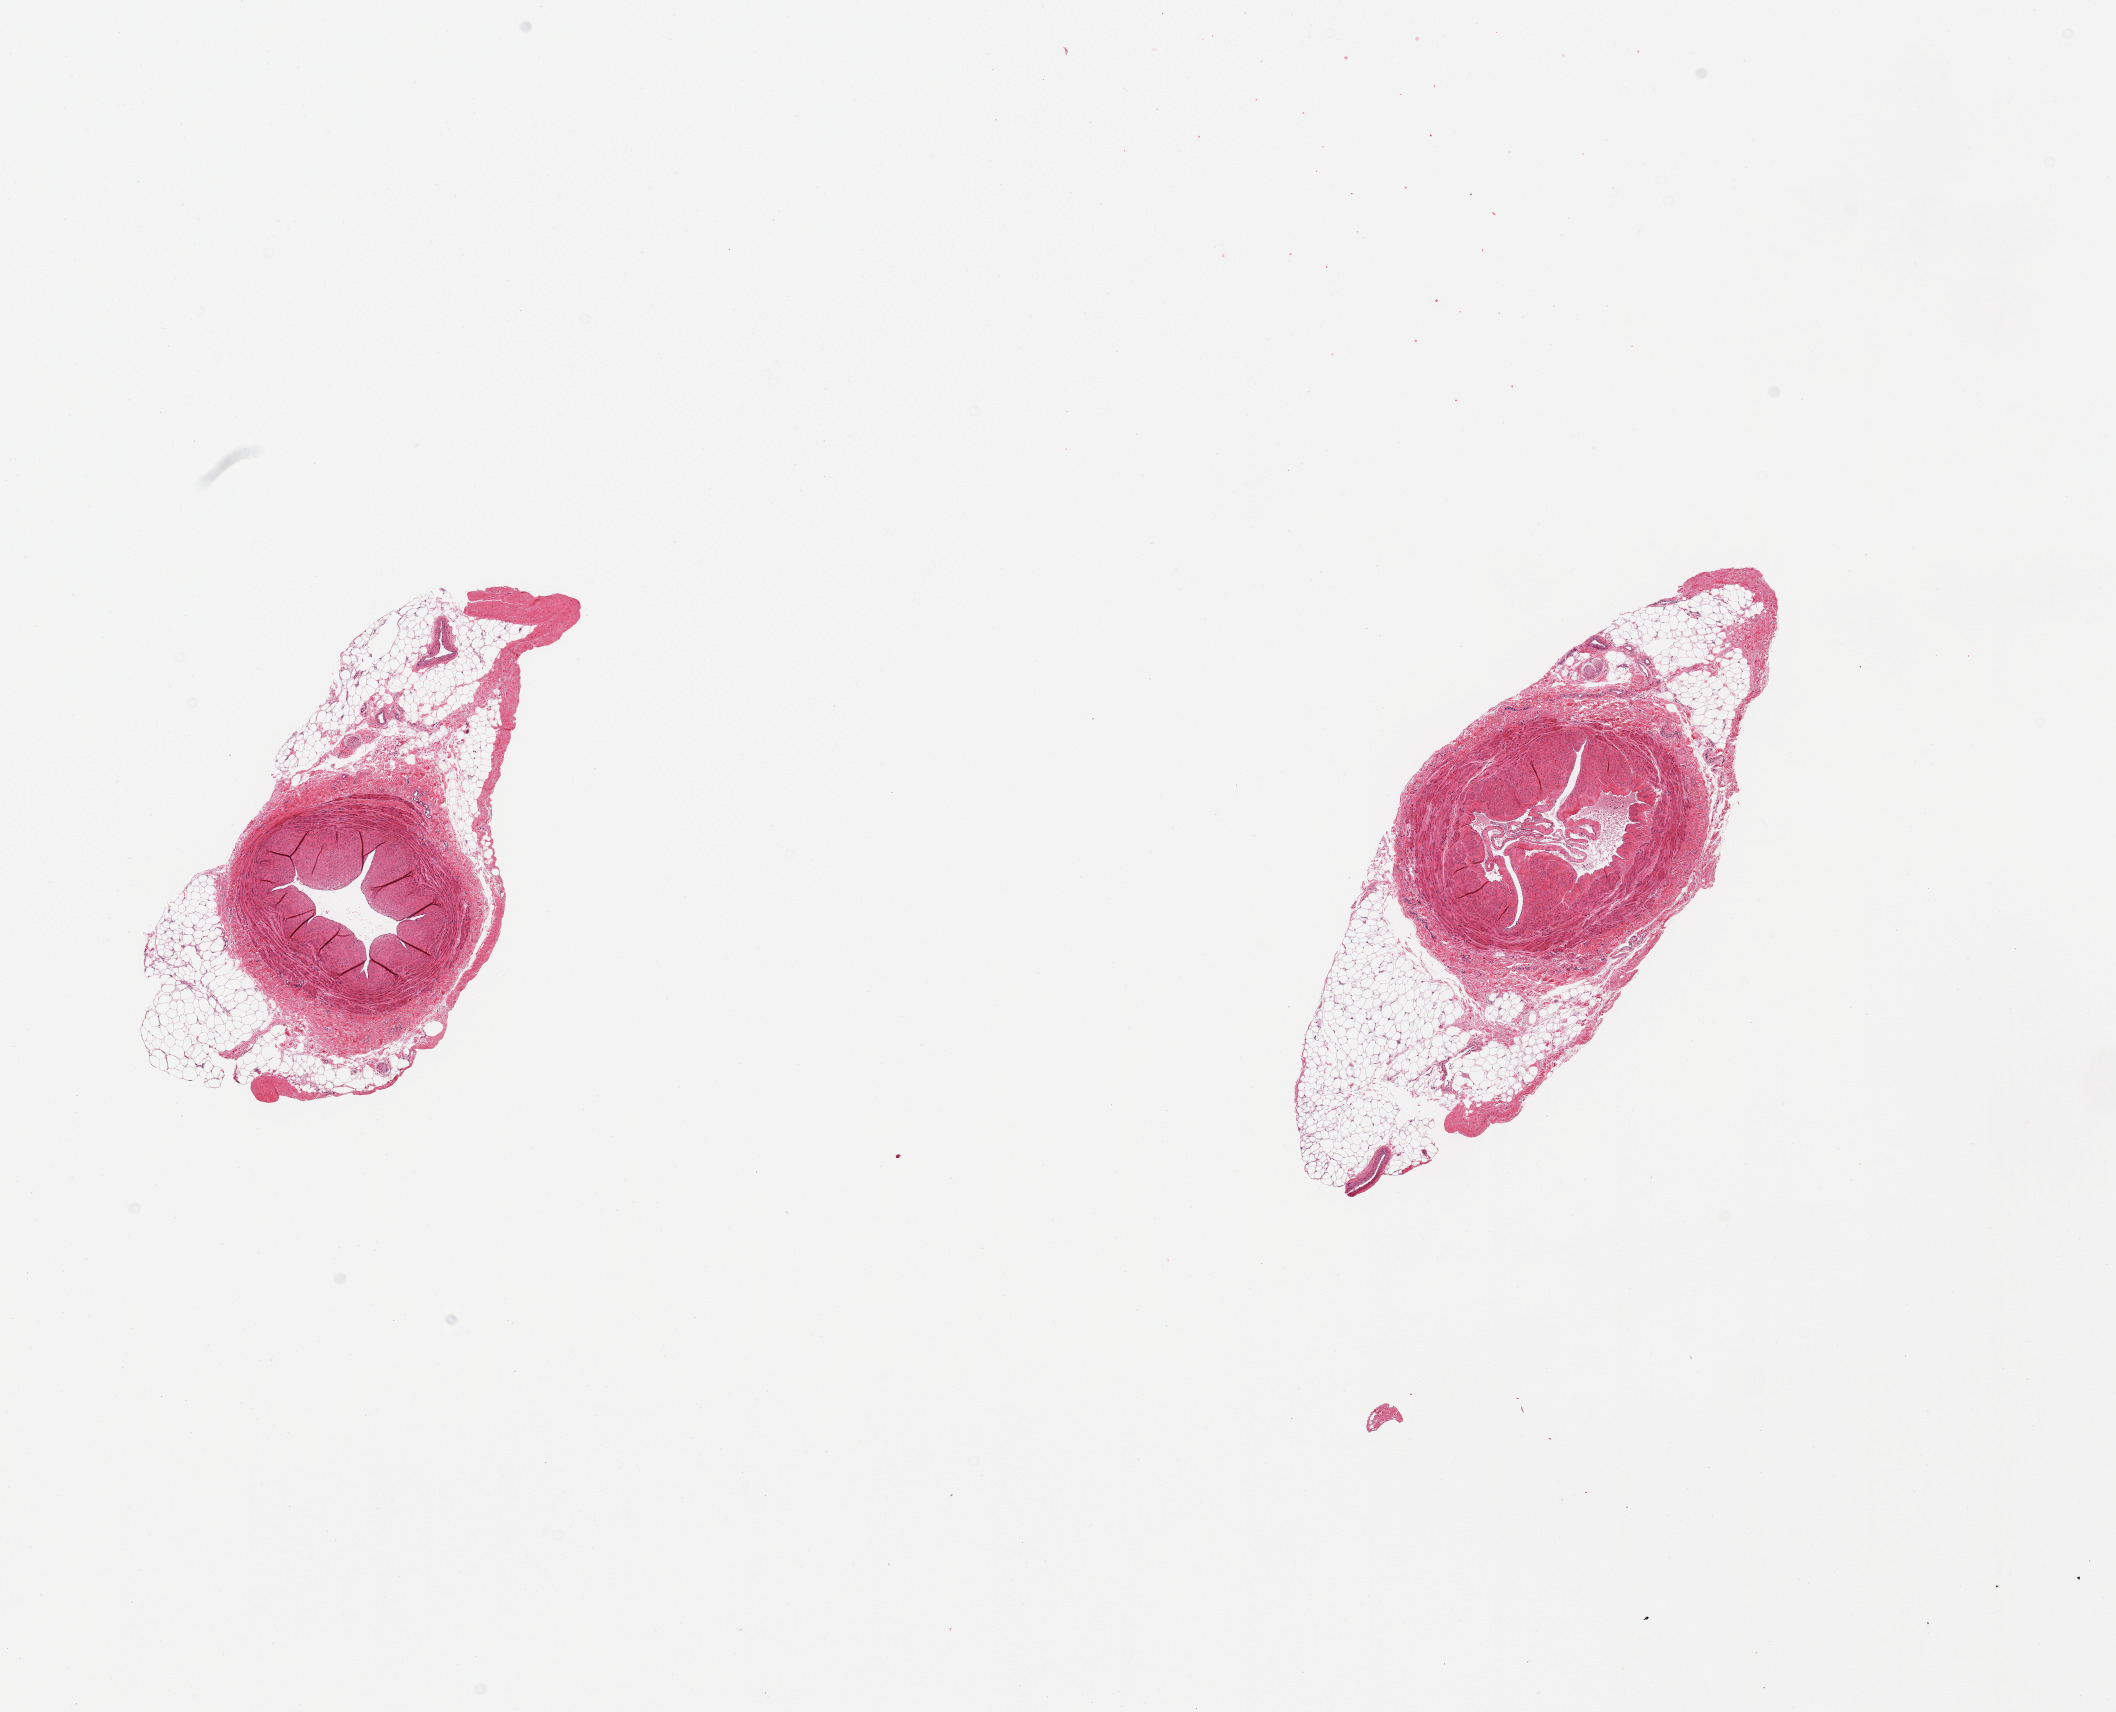
Hematoxylin and eosin (H&E) whole-slide image, brightfield, shown as a low-resolution overview of the whole scanned area (about 16.7 x 13.5 mm, acquisition: 20x scan), PAXgene-fixed, paraffin-embedded tissue, target tissue: tibial artery, tissue donor sample. Female donor.
Reviewer comment on this tissue sample: 2 pieces; abnormal vein, not artery; marked subintimal muscular thickening; up to 1.9 mm external fat; may be related to Buerger's disease.